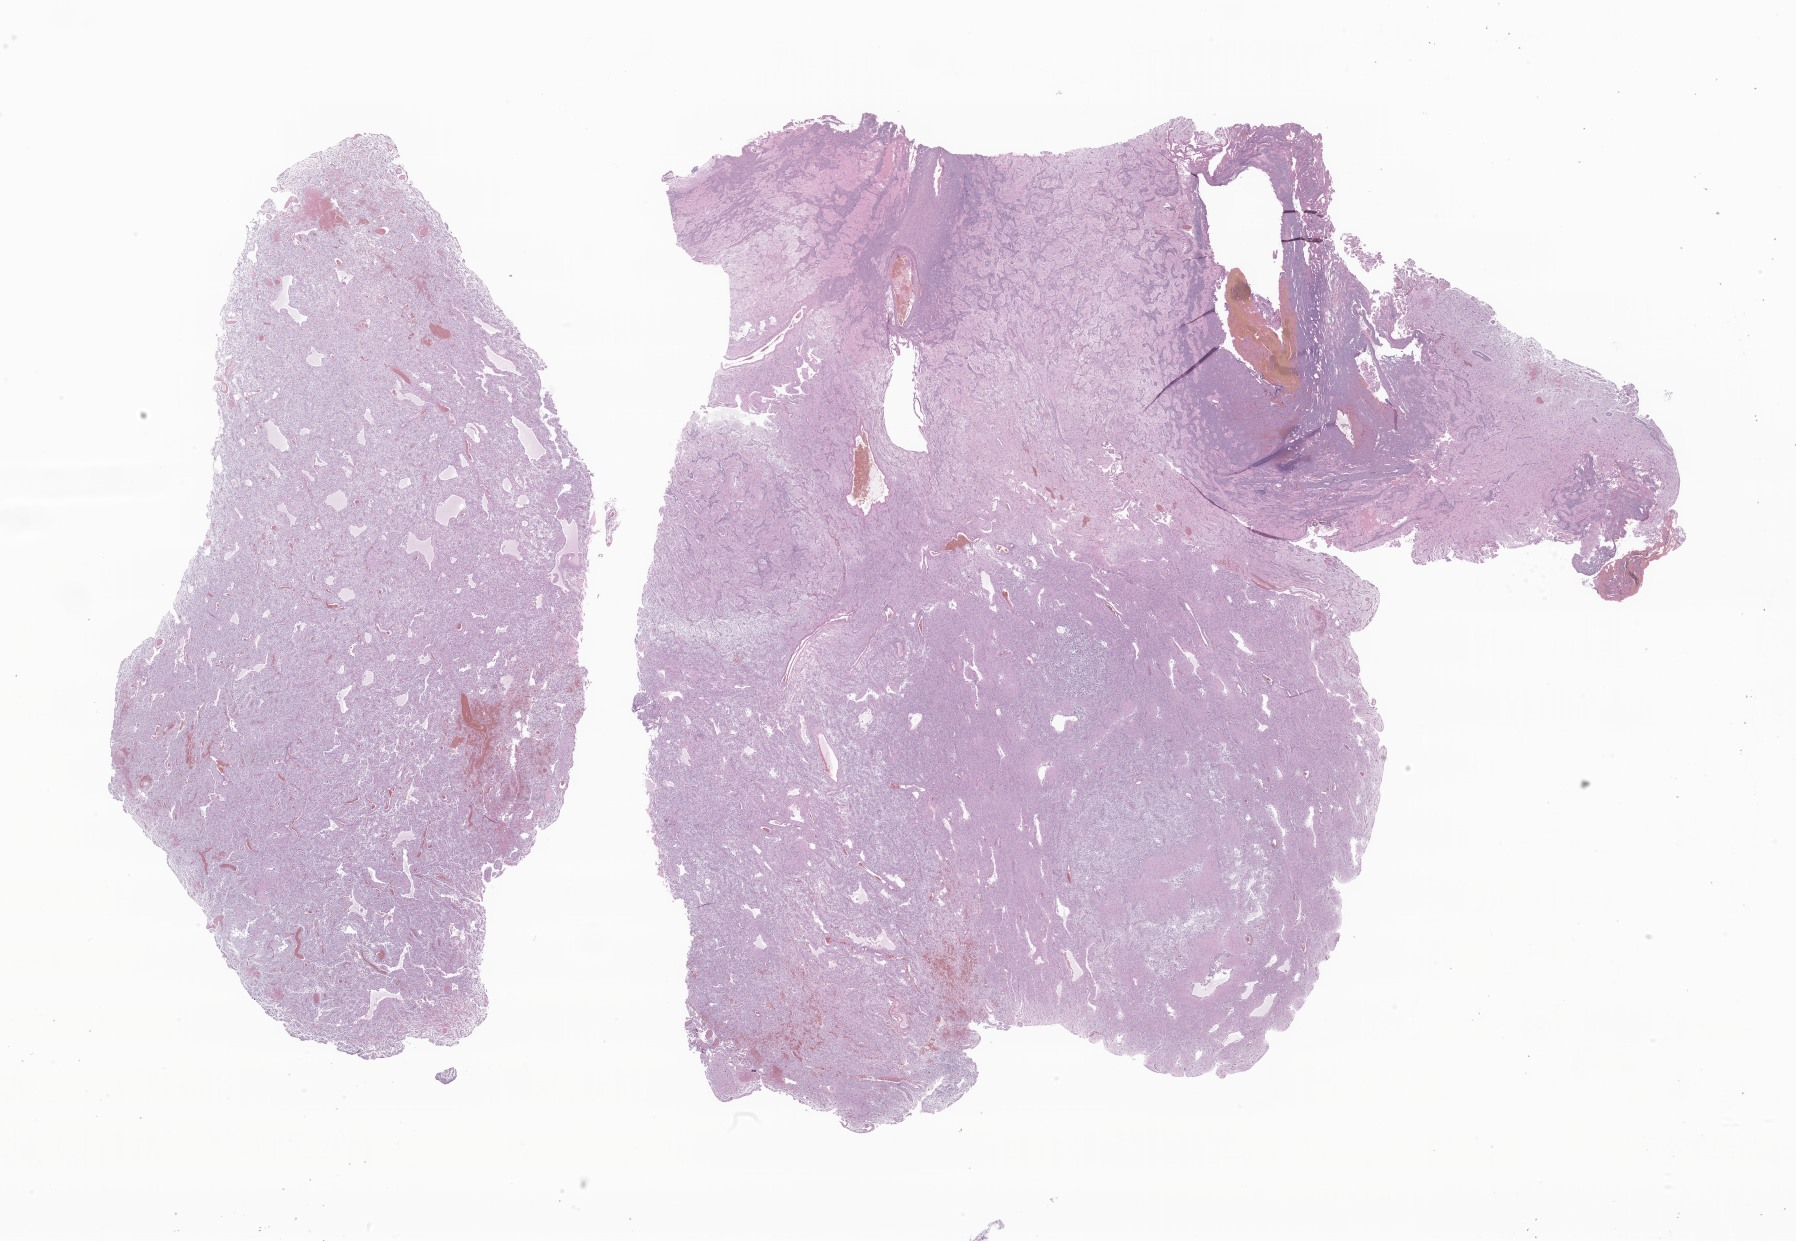
Whole-slide image, H&E stain of tumor tissue from the cerebellum — low-resolution overview of the scanned area, about 30.3 x 20.9 mm; formalin-fixed, paraffin-embedded (FFPE) tissue. Male patient, age 91 months (7 years 7 months).
Diagnosis: Pilocytic astrocytoma.